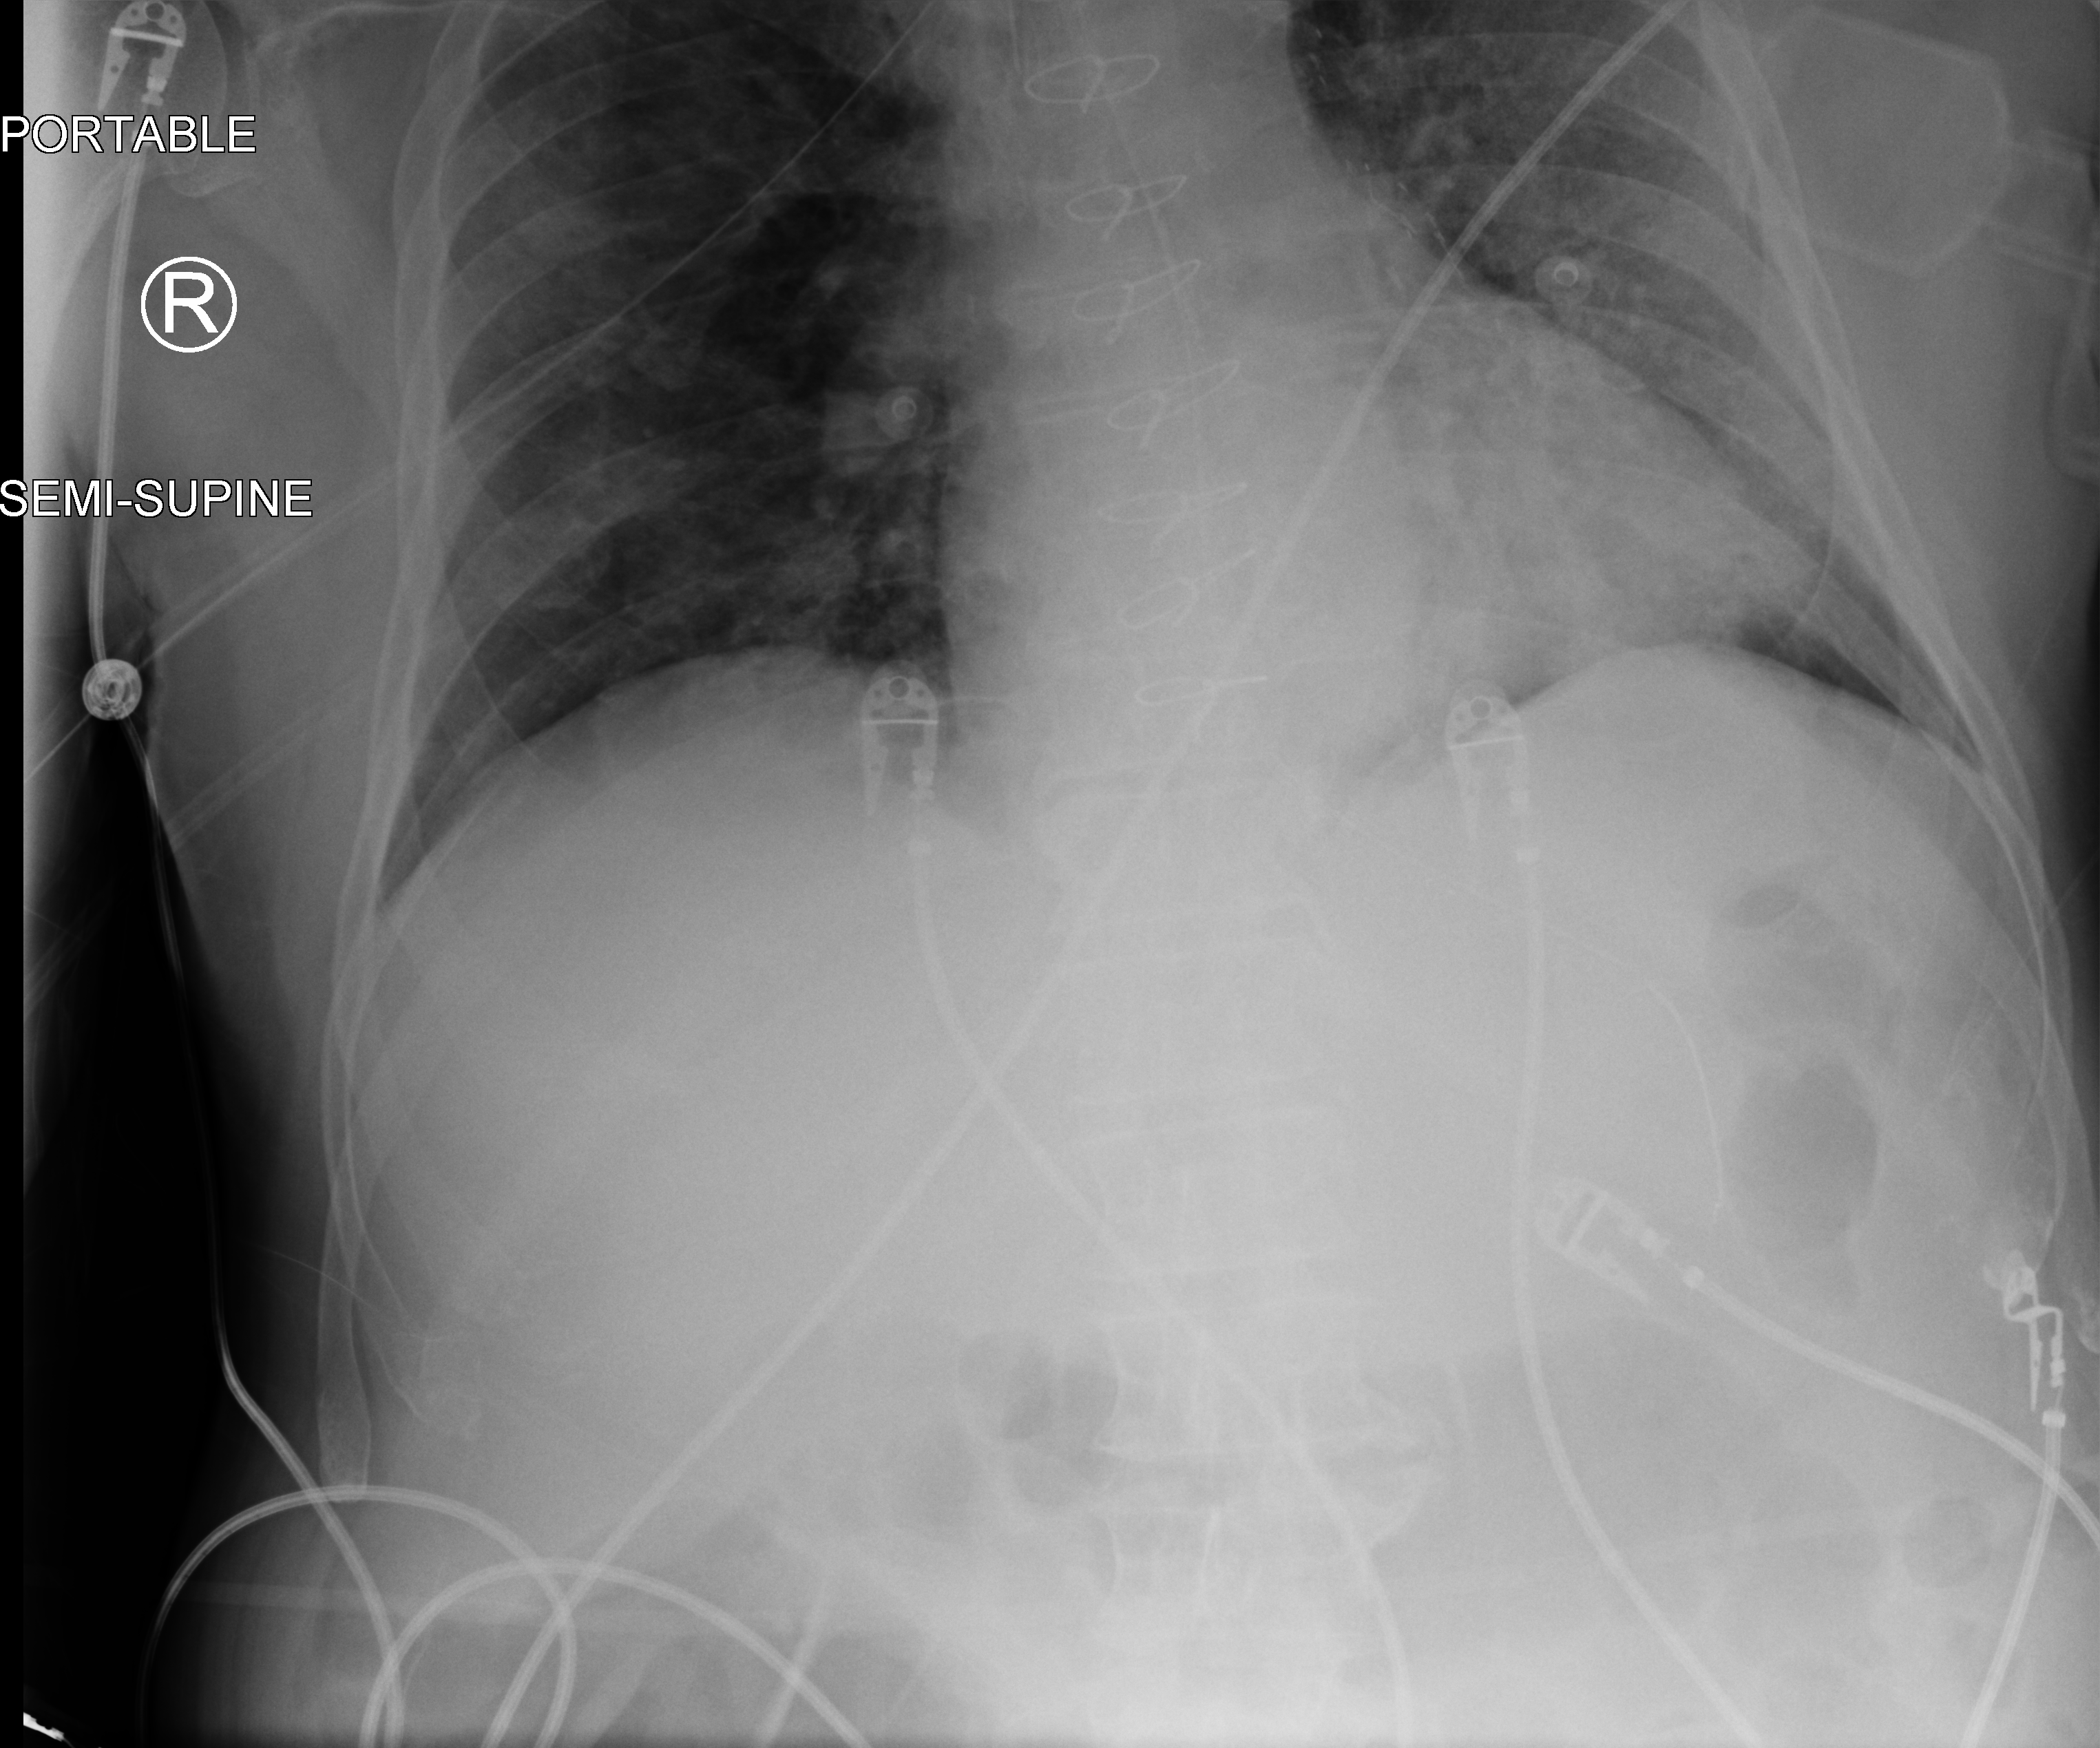
Portable chest radiograph; anteroposterior (AP) projection. Patient hospitalised with COVID-19; male, aged 60–74 years.
From the hospital-stay record, not from the radiograph (when in the stay this image was taken is not recorded): mechanically ventilated during this hospital stay: yes; admitted to intensive care during this hospital stay: yes.